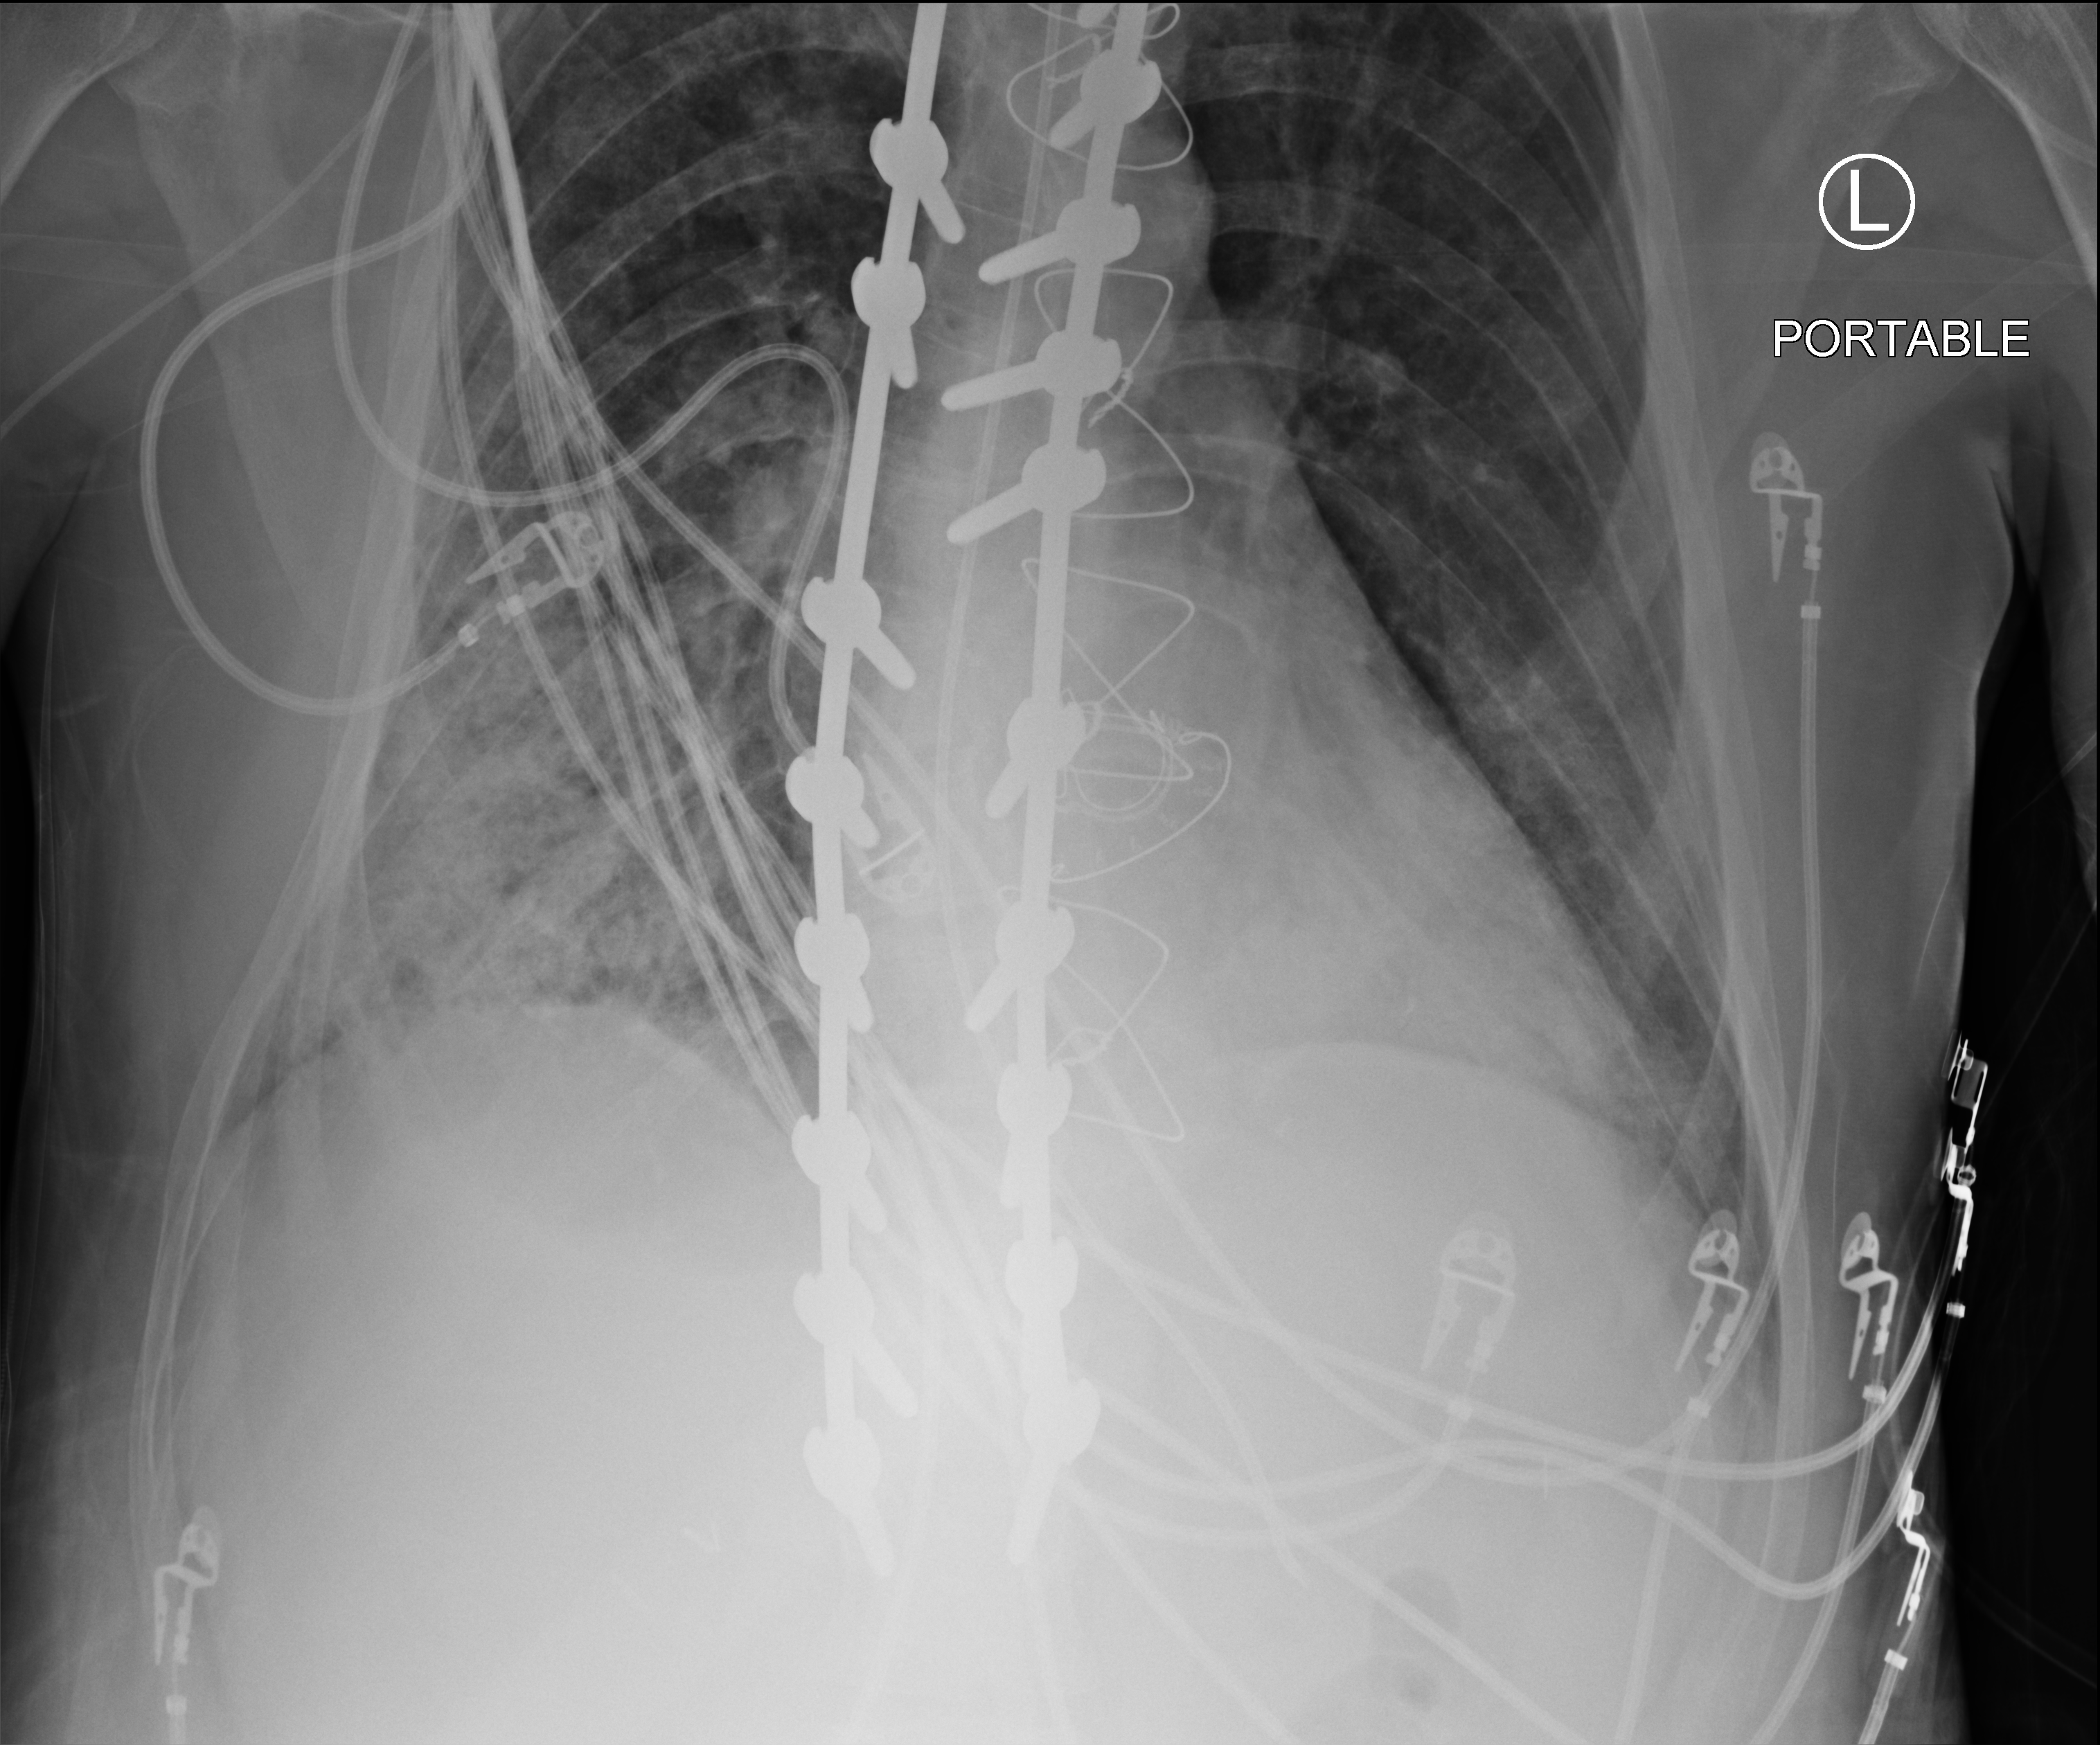
Portable chest radiograph. Patient hospitalised with COVID-19, aged 18–59 years.
From the hospital-stay record, not from the radiograph (when in the stay this image was taken is not recorded): other chronic lung disease (admission record): no; COPD (admission record): no; mechanically ventilated during this hospital stay: yes.